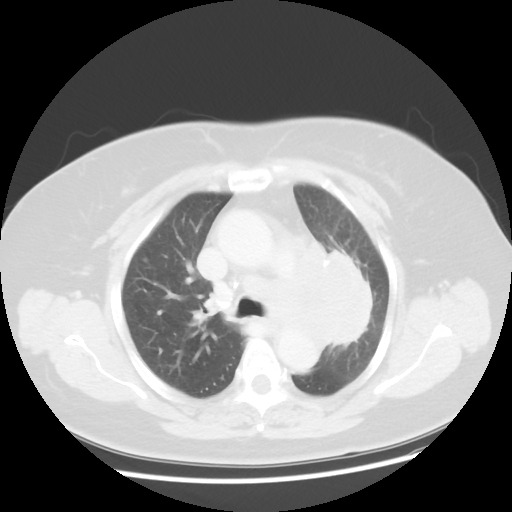
Chest CT, one axial slice. Reconstruction kernel STANDARD. 120 kVp. Lung window (W 1500 / L -600 HU). 5 mm slice thickness. 512 × 512 image matrix. Patient: female, 58 years. Case-level facts recorded for this patient, not image findings: clinical TNM (as recorded): T4 N3 M0; histopathological grade: G3.
Structures marked on this image (rectangle marked by the reading radiologist):
- lung tumour (recorded histology: small cell carcinoma): bounding box <275,226,378,348> (left, top, right, bottom; pixels)